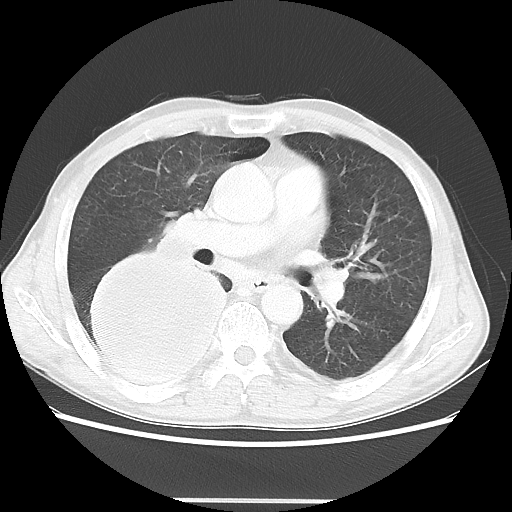
Chest CT, one axial slice. Slice 26 of 48 in the series (ordered by position). Reconstruction kernel LUNG. Lung window (W 1500 / L -600 HU). 512 × 512 image matrix, field of view 361 × 361 mm. Patient: male, 66 years. From the clinical record (not read from this slice): clinical TNM (as recorded): T4 N1 M1; histopathological grade: G3.
Annotated regions visible in this slice (bounding box drawn by a radiologist):
- lung tumour (recorded histology: small cell carcinoma): bounding box [x1, y1, x2, y2] px = [85, 246, 234, 389]